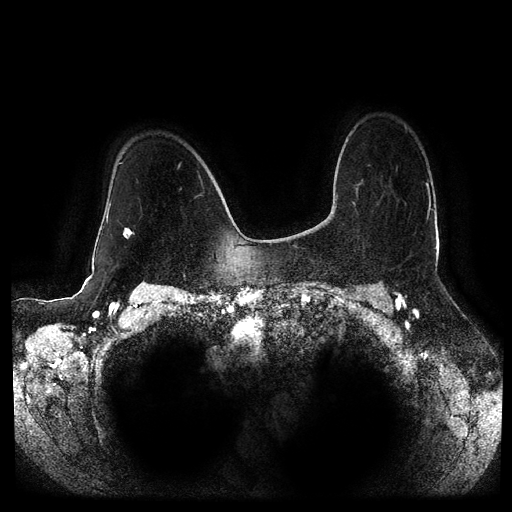
Breast MRI (dynamic contrast-enhanced, multi-phase), one axial slice. Position 74 of 116 along the scan axis. Dynamic contrast-enhanced series, time point 2 of 5 at this slice position (early post-contrast). 1.5 T. TE 2.6 ms, TR 5.2 ms. 2 mm slice thickness. 512 × 512 image matrix, field of view 380 × 380 mm. Patient: female, 53 years.
Structures marked on this image (semi-automatic segmentation, software-assisted and operator-edited):
- breast lesion (labelled 'tumour' in the annotation; benign lesions carry a separate 'benign' label): bounding box <123,228,134,239> (left, top, right, bottom; pixels)